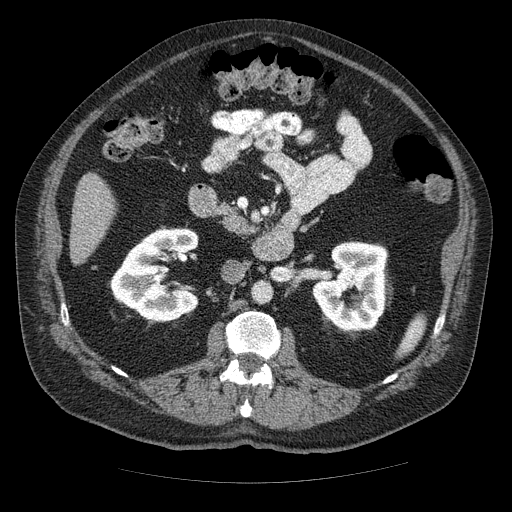
Contrast-enhanced abdominal CT (liver protocol), one axial slice. Slice 11 of 85 in the series (ordered by position). Reconstruction kernel STANDARD. Soft-tissue window (W 400 / L 40 HU). 2.5 mm slice thickness. 512 × 512 image matrix, field of view 420 × 420 mm. Case-level facts recorded for this patient, not image findings: diagnosis: hepatocellular carcinoma (patient treated with transarterial chemoembolisation; whether this scan precedes or follows treatment is not stated here); TNM stage (as recorded): Stage-IIIA; Child-Pugh class: A; tumour nodularity: multinodular; tumour size: 7 cm.
Annotated regions visible in this slice (semi-automatically segmented with operator editing):
- liver parenchyma outside the tumour (the mass and vessels are separate outlines, so this box may not span the whole liver): bounding box (x1, y1, x2, y2) in pixels: (70, 172, 116, 264)